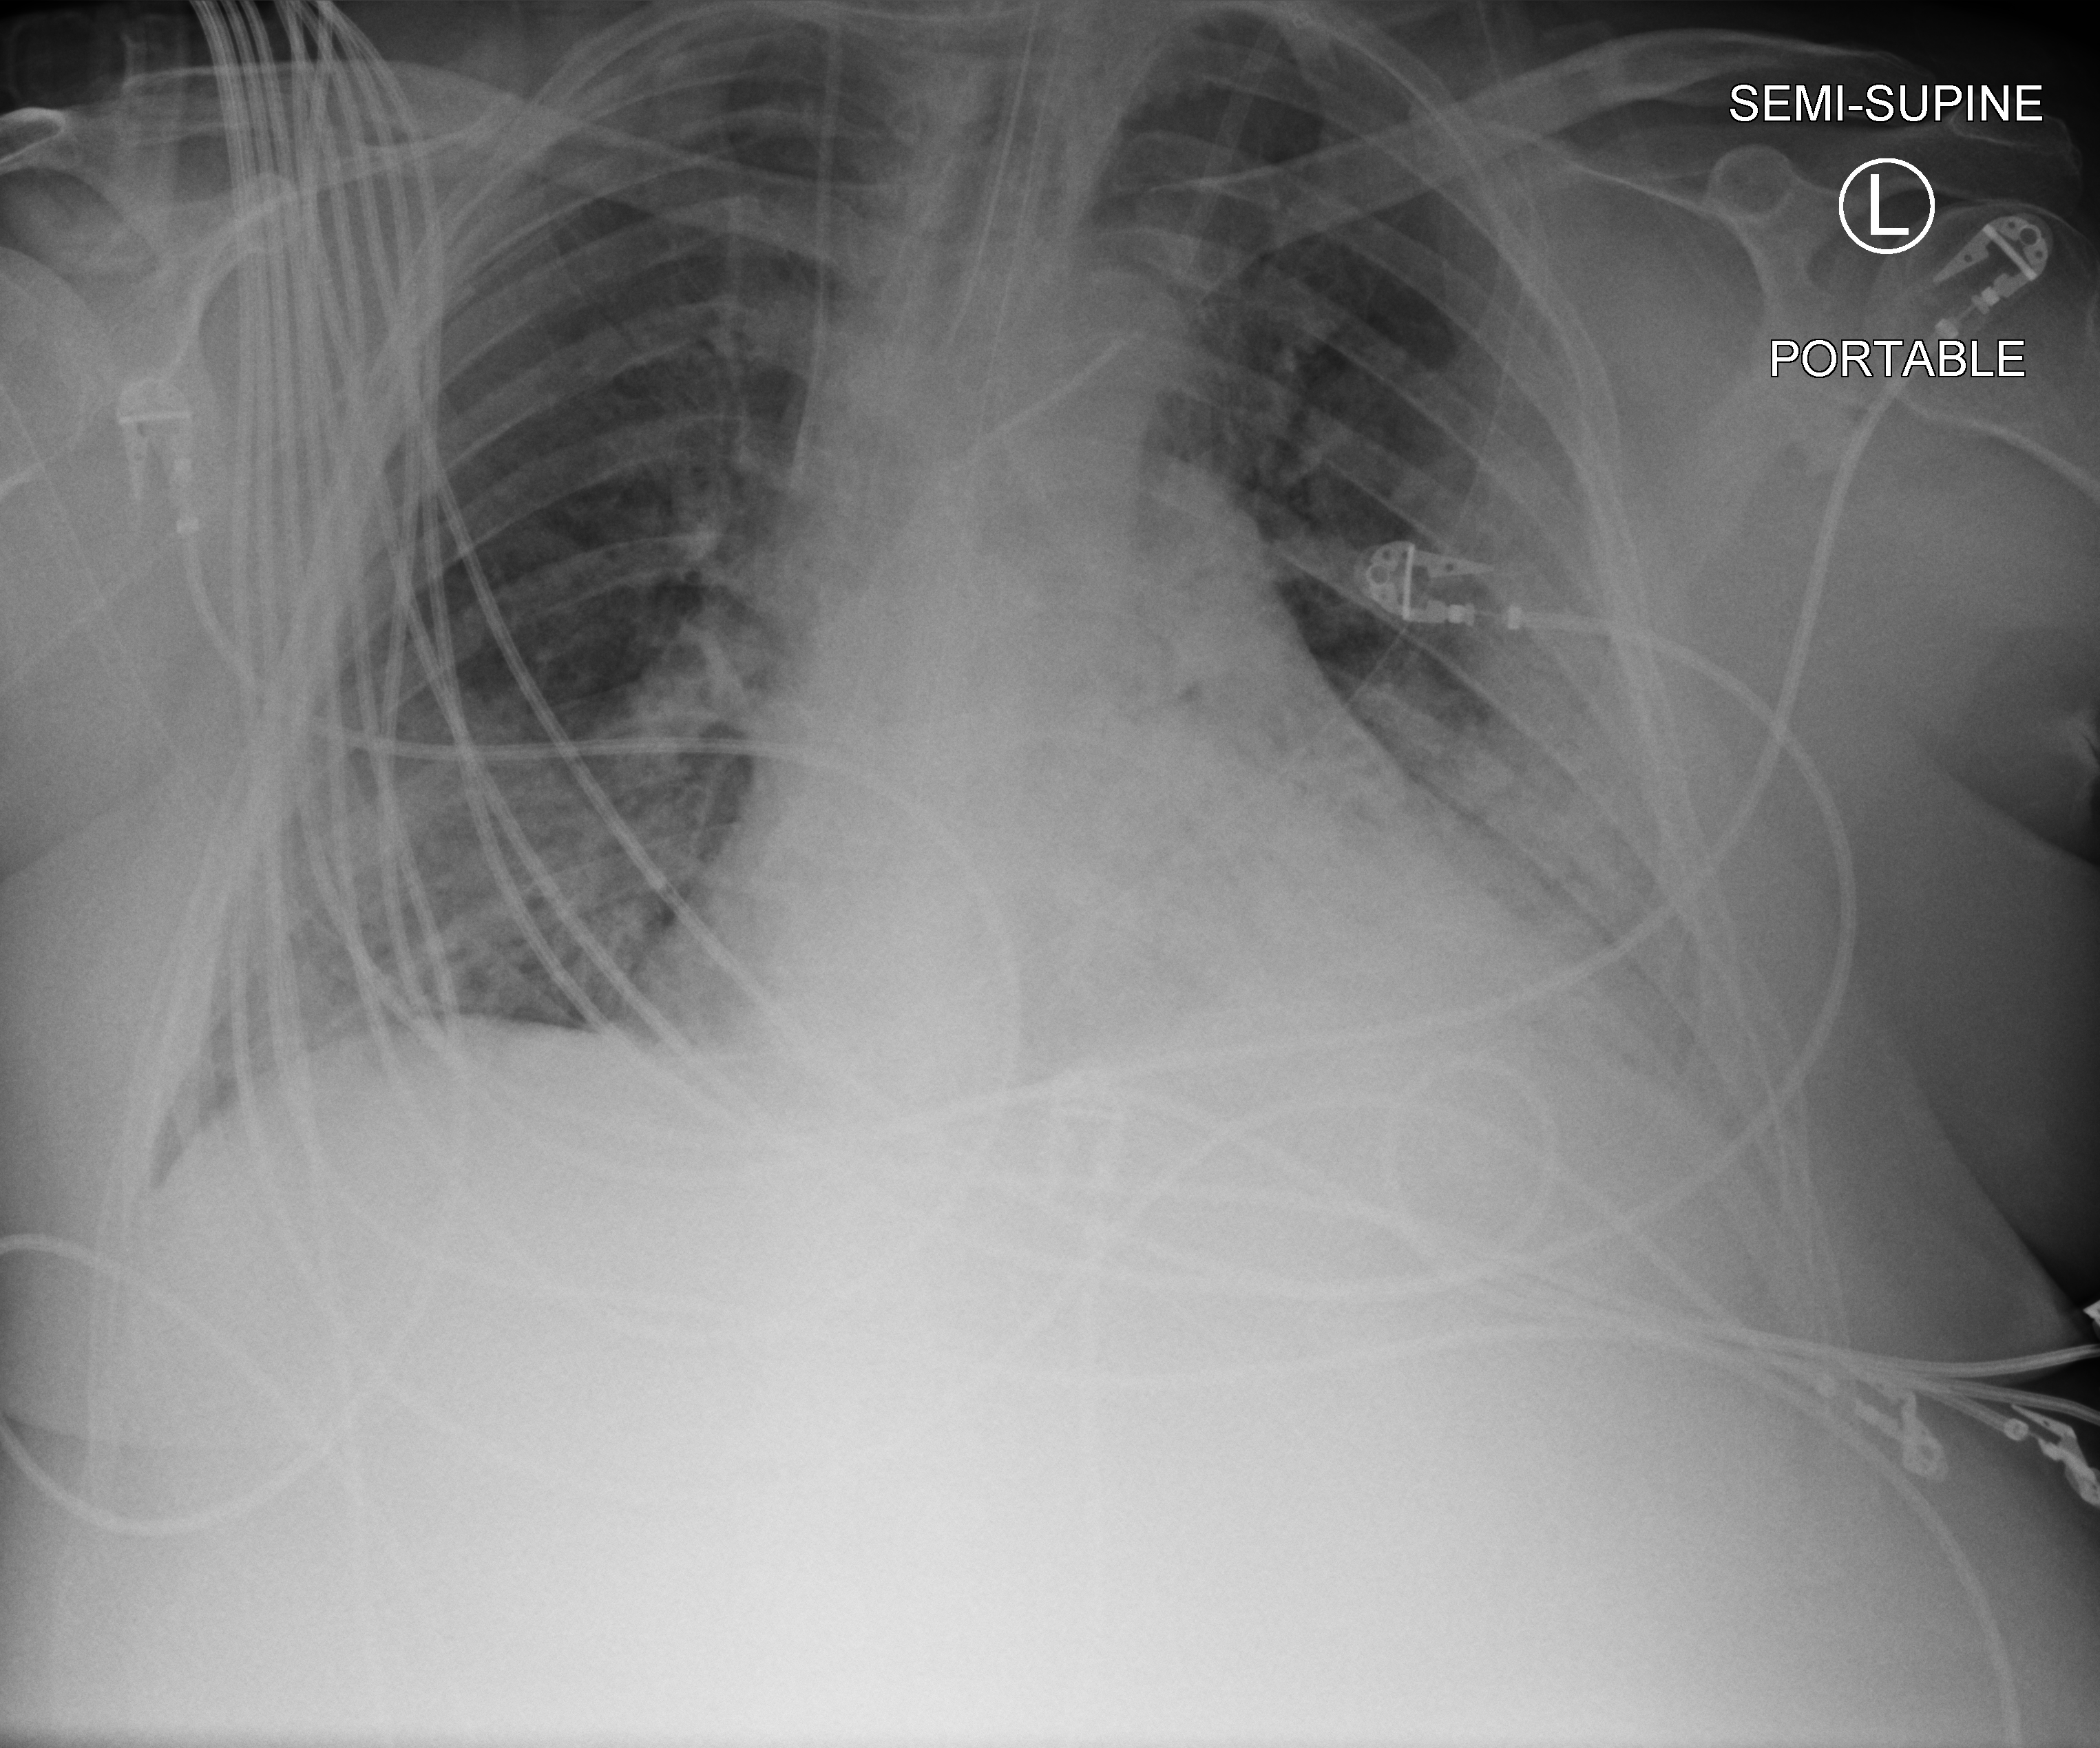
Bedside chest radiograph (computed radiography); anteroposterior (AP) projection. Male patient hospitalised with COVID-19, age 18–59 years.
Admission-level facts for this patient (not findings on this image; timing relative to this image not recorded):
- hypertension (admission record): yes